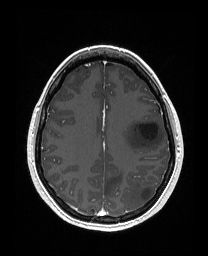
Brain MRI from a brain-tumour surgery series, one axial slice. Slice 109 of 176 in the series (ordered by position). T1-weighted post-contrast. 1 mm slice thickness. 208 × 256 image matrix, field of view 203 × 250 mm. Case-level facts recorded for this patient, not image findings: histopathology: Astrocytoma; WHO grade: 3; IDH mutation: yes; tumour location: Left Frontal.
Annotated regions visible in this slice (manually delineated by an expert):
- tumour: bounding box (x1, y1, x2, y2) in pixels: (122, 120, 164, 154)